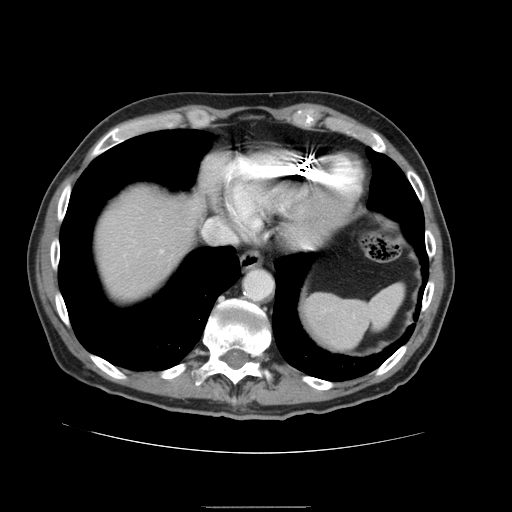
Contrast-enhanced abdominal CT, one axial slice; slice 134 of 168 in the series (ordered by position); intravenous contrast given; soft-tissue window (W 400 / L 40 HU); 2.5 mm slice thickness; 512 × 512 image matrix, field of view 386 × 386 mm. Male patient, age 74 years. Case-level facts recorded for this patient, not image findings: diagnosis: colorectal cancer liver metastases, imaged before liver resection; multiple liver metastases: no; largest metastasis: 14.5 cm.
Structures marked on this image (manually delineated by an expert):
- liver: bounding box (x1, y1, x2, y2) in pixels: (92, 183, 205, 307)
- planned liver remnant (the part of the liver to remain after resection): (93, 182, 204, 306)